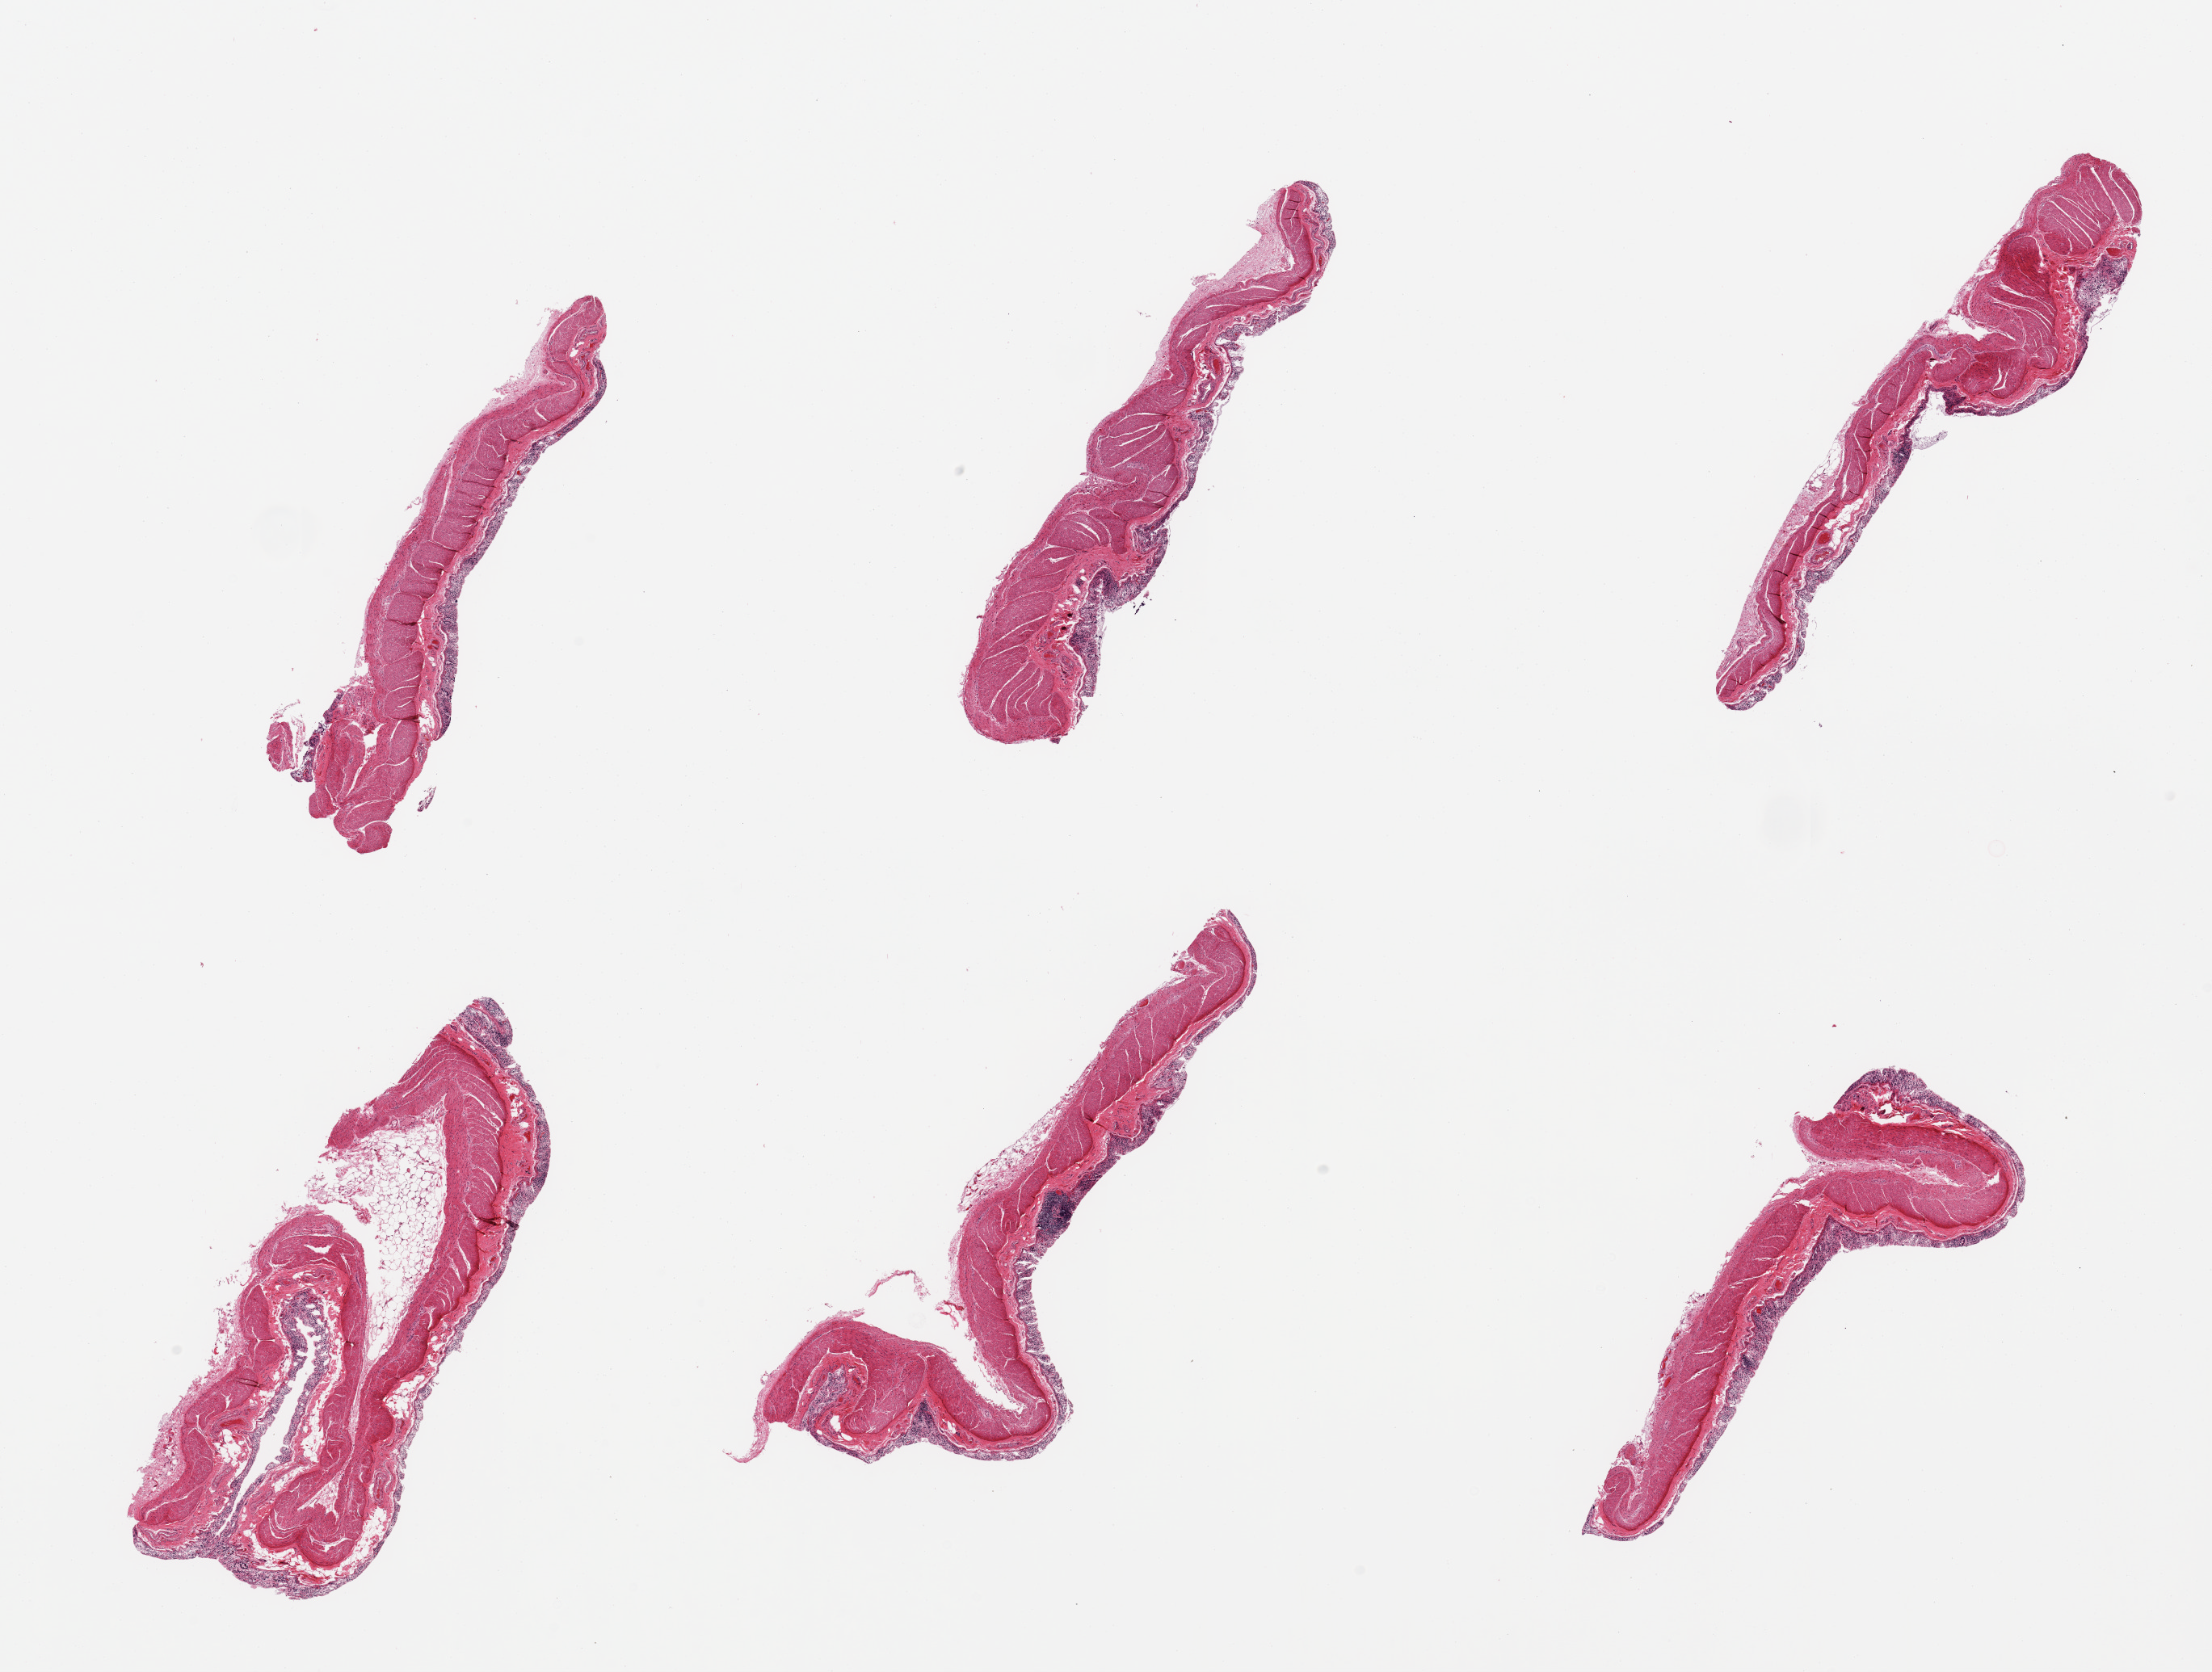
Digitized hematoxylin and eosin (H&E)-stained section, brightfield, shown as a low-resolution overview of the whole scanned area (about 21.7 x 16.4 mm, acquisition: 20x scan). PAXgene-fixed paraffin-embedded (PFPE) section. Sampled site (target tissue): transverse colon. Donor tissue sample.
Reviewer comment on this tissue sample: 6 pieces; mucosa autolyzed, muscle intact.